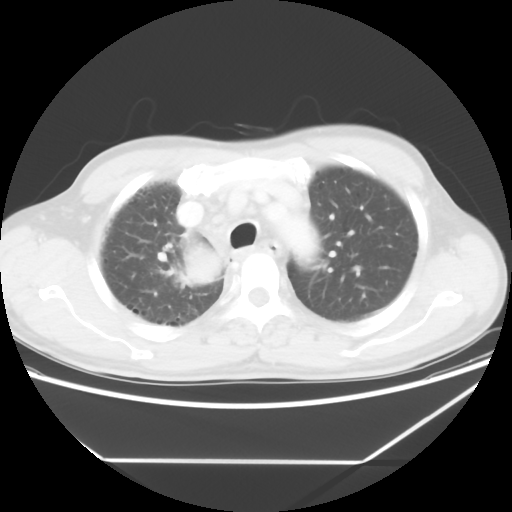
Chest CT, one axial slice; position 47 of 60 along the scan axis; reconstruction kernel STANDARD; 120 kVp; lung window (W 1500 / L -600 HU); 5 mm slice thickness; 512 × 512 image matrix. Male patient, age 58 years. Case-level facts recorded for this patient, not image findings: clinical TNM (as recorded): T2 N2 M0.
Outlined on this slice (bounding box drawn by a radiologist):
- lung tumour (recorded histology: squamous cell carcinoma): bounding box [x1, y1, x2, y2] px = [166, 241, 225, 298]